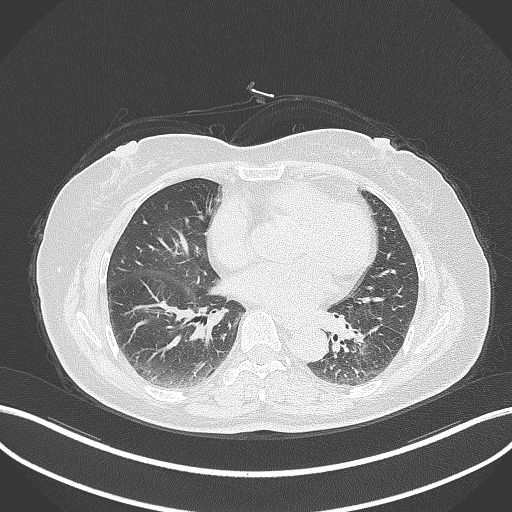
Chest CT, one axial slice; position 166 of 311 along the scan axis; reconstruction kernel B70f; 120 kVp; lung window (W 1500 / L -600 HU); 1 mm slice thickness; 512 × 512 image matrix, field of view 400 × 400 mm. Patient: female, 59 years. Case-level facts recorded for this patient, not image findings: clinical TNM (as recorded): T2a N0 M0; histopathological grade: G2-3.
Structures marked on this image (bounding box drawn by a radiologist):
- lung tumour (recorded histology: adenocarcinoma): bounding box (x1, y1, x2, y2) in pixels: (351, 317, 385, 349)